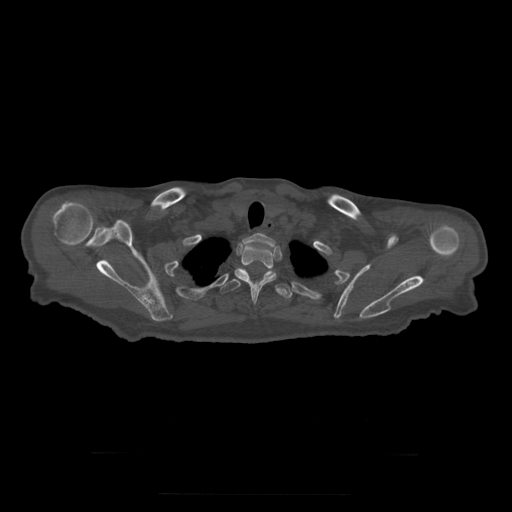
CT including the spine, one axial slice. Slice 270 of 397 in the series (ordered by position). Reconstruction kernel STANDARD. 120 kVp. Bone window (W 1800 / L 400 HU). 512 × 512 image matrix. Patient age 73 years. Case-level facts recorded for this patient, not image findings: primary cancer: prostate.
Annotated regions visible in this slice (semi-automatically segmented with operator editing):
- T1 vertebra: bounding box (x1, y1, x2, y2) in pixels: (243, 233, 276, 247)
- T2 vertebra: (235, 244, 277, 303)
- T3 vertebra: (220, 268, 293, 299)